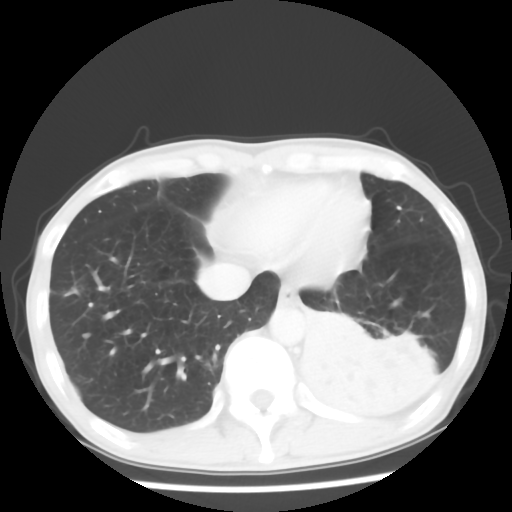
Chest CT, one axial slice; slice 14 of 64 in the series (ordered by position); lung window (W 1500 / L -600 HU); 512 × 512 image matrix, field of view 313 × 313 mm. Male patient, age 68 years. Case-level facts recorded for this patient, not image findings: clinical TNM (as recorded): T4 N0 M0.
Structures marked on this image (bounding box drawn by a radiologist):
- lung tumour (recorded histology: squamous cell carcinoma): bounding box <288,300,447,434> (left, top, right, bottom; pixels)